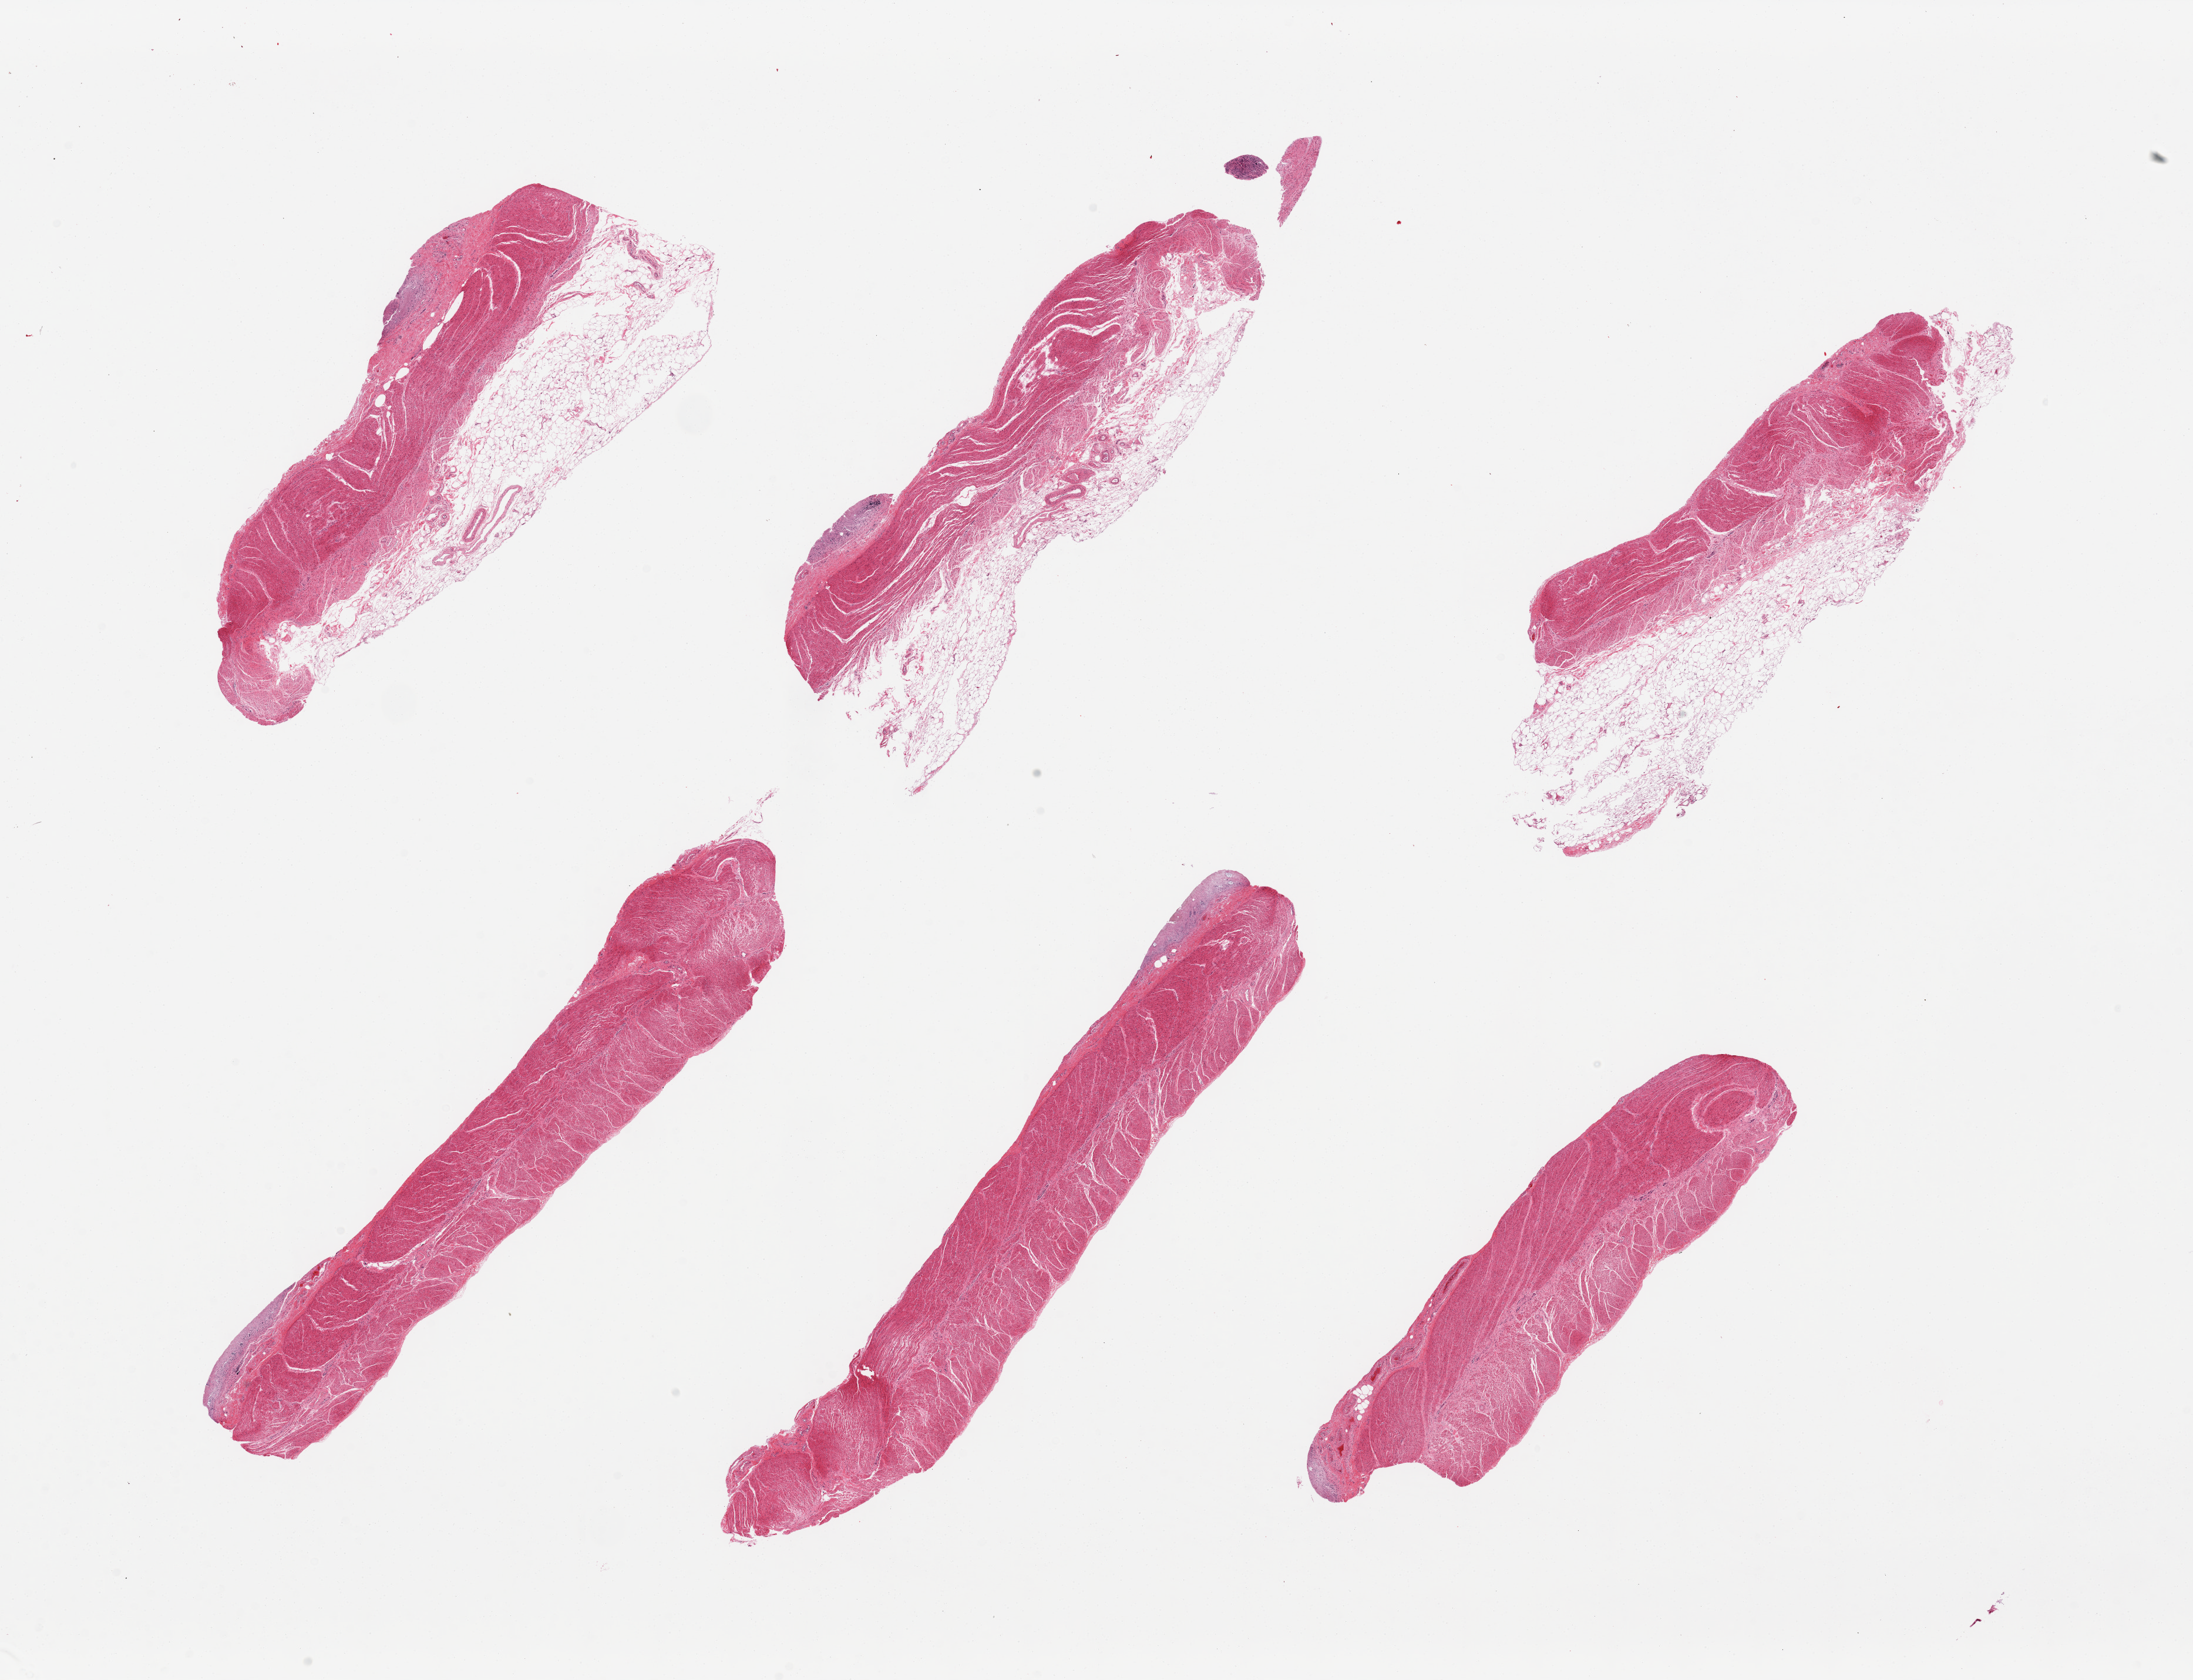
Digitized haematoxylin and eosin-stained section, low-resolution overview of the scanned area, about 29.5 x 22.6 mm (slide scanned at 20x); PAXgene-fixed paraffin-embedded (PFPE) section; section of sigmoid colon (target tissue); donor tissue sample. Donor: male.
Reviewer comment on this tissue sample: 6 pieces; adherent layer fat/seroa in 3 up to ~2mm thick; trace residual completely autolyzed mucosa.